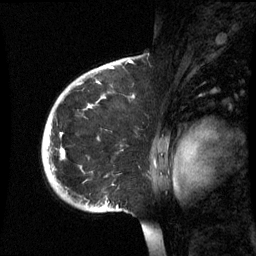
Breast MRI (dynamic contrast-enhanced), one sagittal slice. Slice 44 of 60 in the series (ordered by position). Dynamic contrast-enhanced series, image 2 of 3 at this slice position (ordered by acquisition). 1.5 T. TE 4.2 ms, TR 8.9 ms. 2.6 mm slice thickness. 256 × 256 image matrix, field of view 220 × 220 mm. Patient: female, 35 years. Case-level facts recorded for this patient, not image findings: setting: breast cancer imaged before/during neoadjuvant chemotherapy; receptor status: HR-positive, HER2-negative.
Annotated regions visible in this slice (semi-automatic segmentation, software-assisted and operator-edited):
- analysis volume of interest (the breast-tissue region the enhancement analysis was run in; not a lesion): box from (x=42, y=74) to (x=160, y=213) px
- tumour enhancement mask (voxels above the 70 % enhancement threshold inside the analysis volume of interest): (x=62, y=104)–(x=90, y=157)